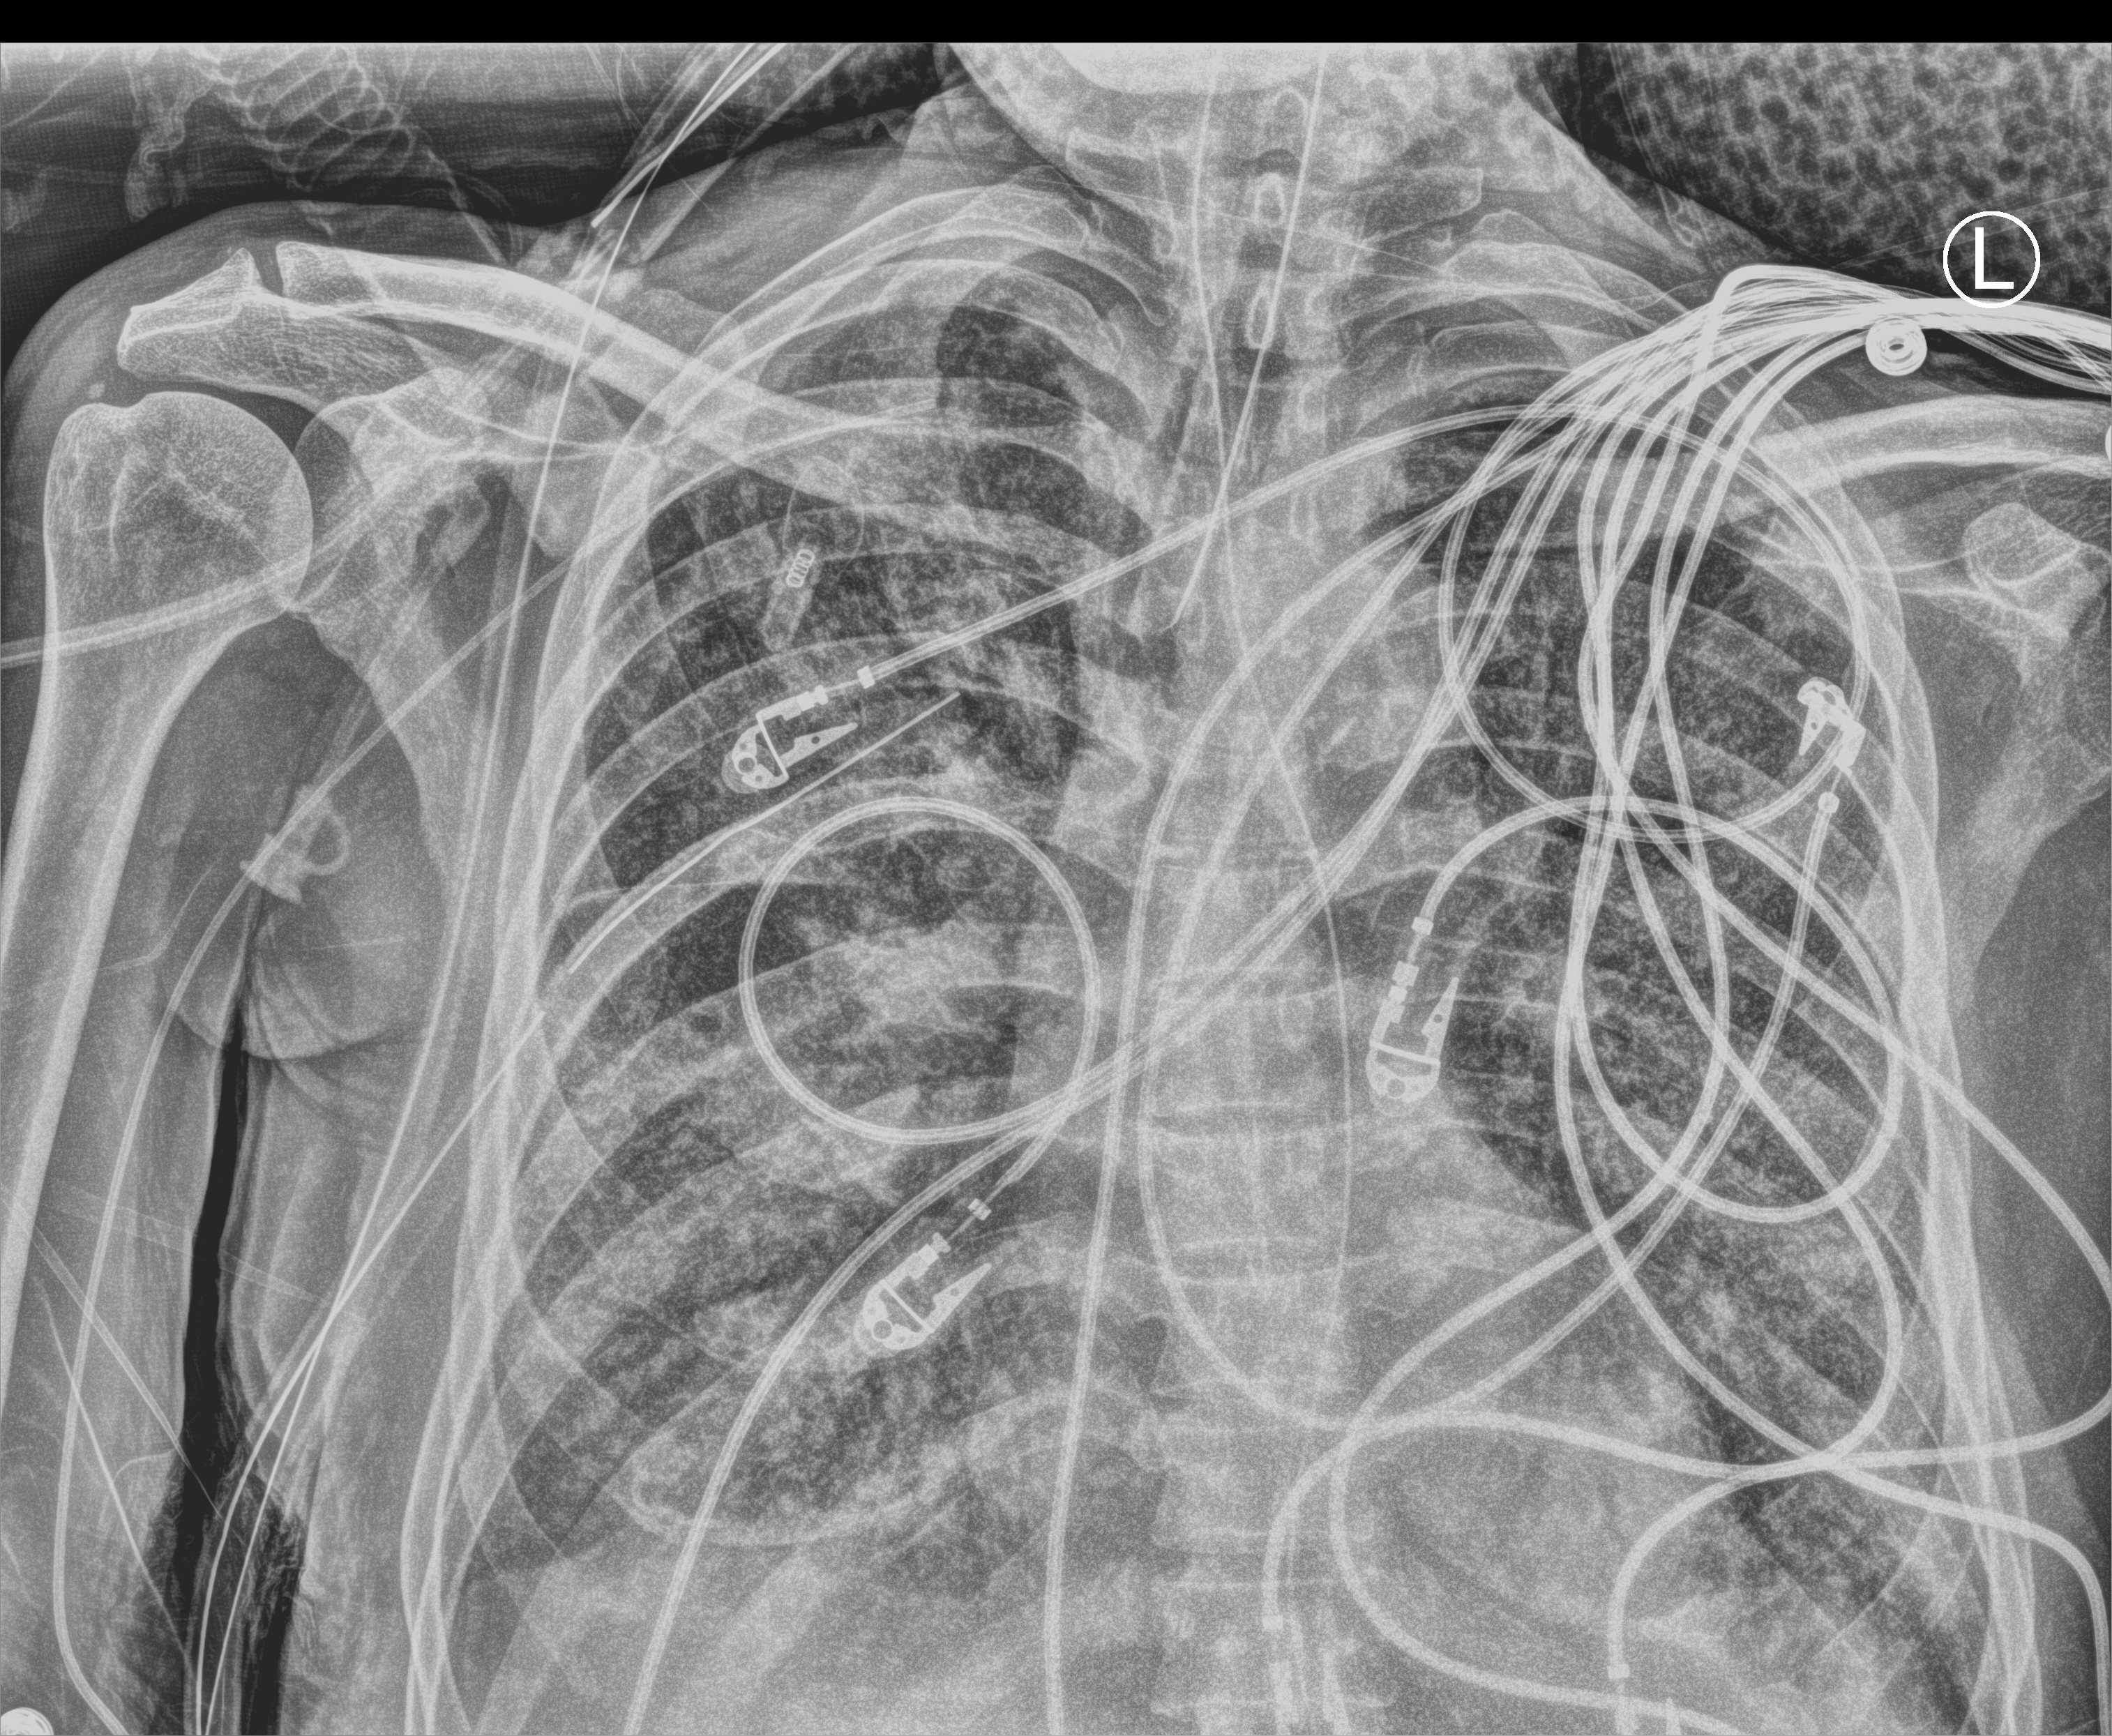
Bedside chest radiograph (computed radiography); anteroposterior (AP) projection. Male patient hospitalised with COVID-19, age 60–74 years.
Admission-level facts for this patient (not findings on this image; timing relative to this image not recorded):
- admitted to intensive care during this hospital stay: yes